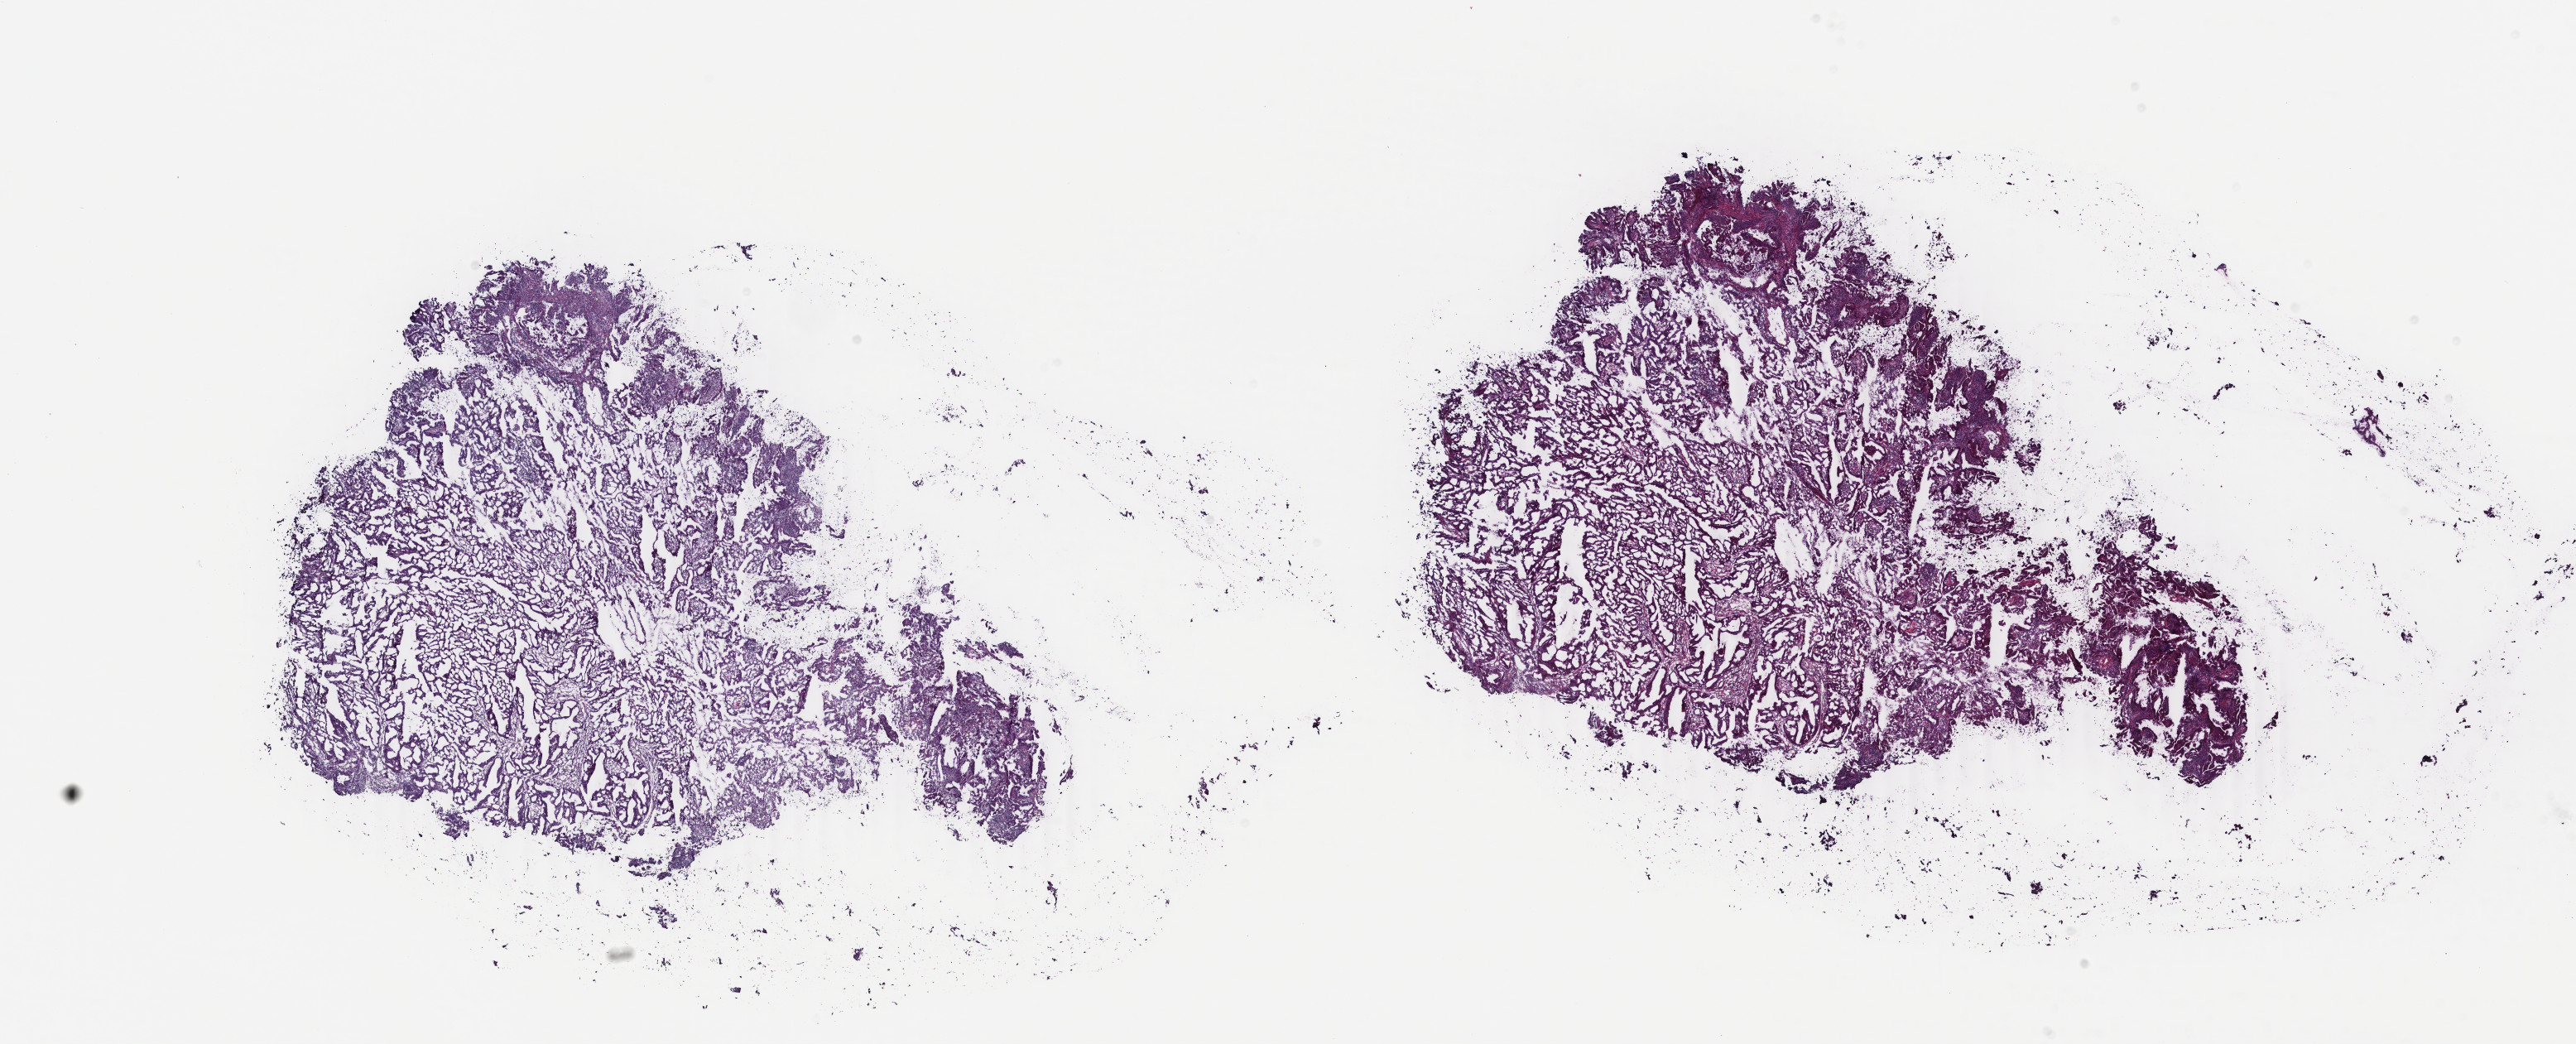
Whole-slide histology image, Hematoxylin and eosin (H&E) stained — low-resolution overview of the scanned area, about 24.7 x 10.0 mm; frozen section; uterus, primary tumour sample. Female patient; age at initial diagnosis 69 years. Histologic grade: G1 (well differentiated). Pathologist review of this section (percent, as recorded): tumour cells 70%, tumour nuclei 75%, normal cells 0%, stromal cells 25%, necrosis 5%. Infiltration values recorded for this section: lymphocyte infiltration 30%, monocyte infiltration 2%, neutrophil infiltration 0%.
FIGO stage: IA. Pathologic diagnosis: Endometrioid adenocarcinoma, NOS (endometrium).